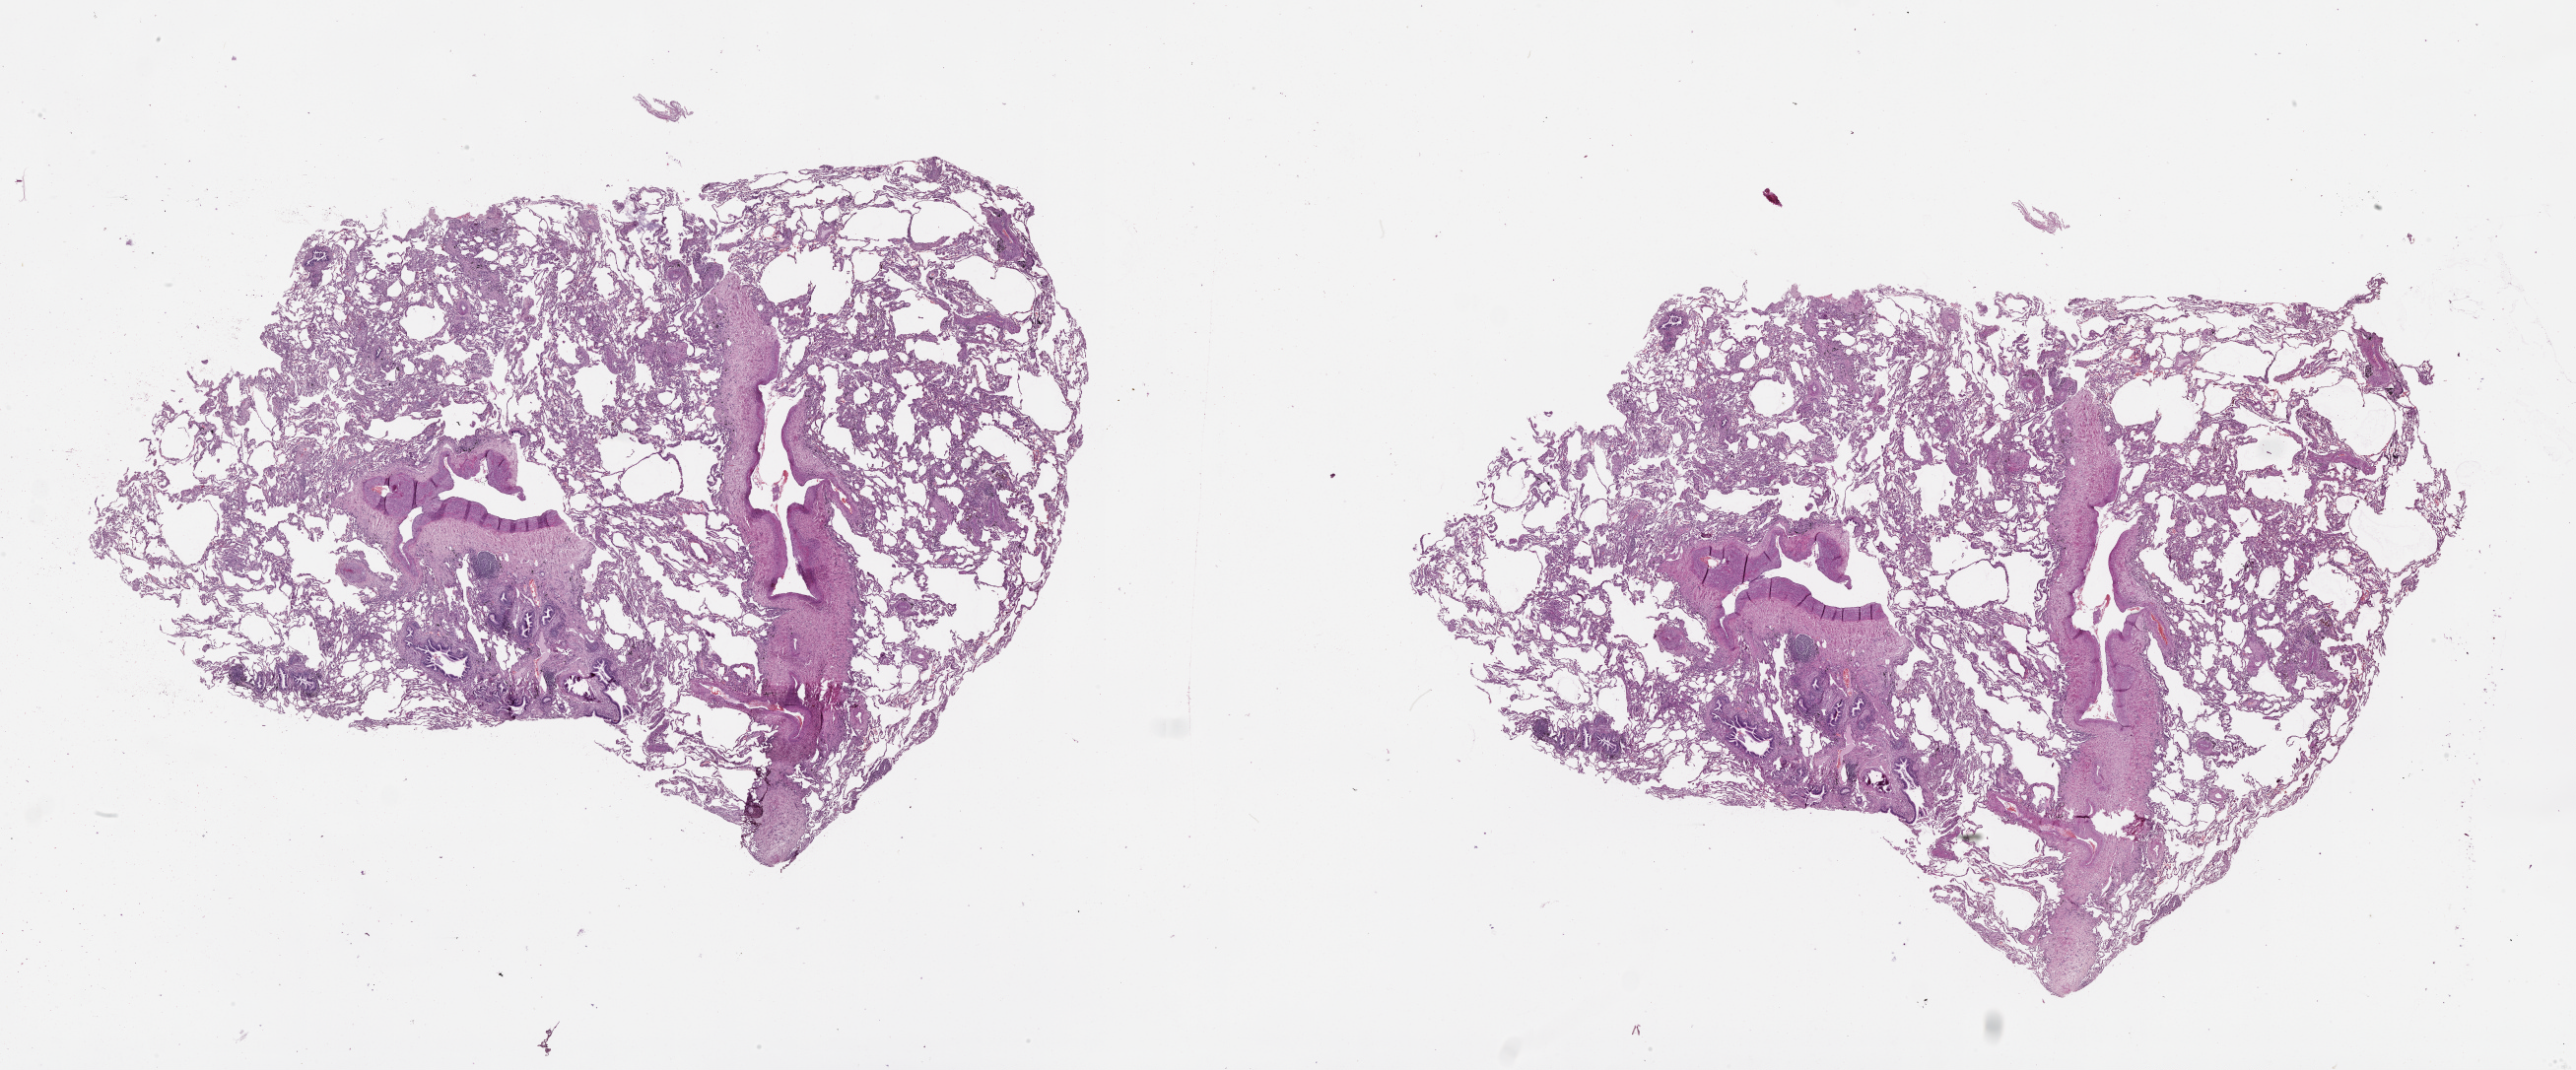
Whole-slide histology image, Hematoxylin and eosin (H&E) stained, low-resolution overview of the scanned area, about 42.1 x 17.5 mm, lung, normal (non-tumour) tissue. Male, 72 y/o.
This section: normal (non-tumour) tissue from the same patient. Patient diagnosis (cohort enrolment): squamous cell carcinoma (lung).